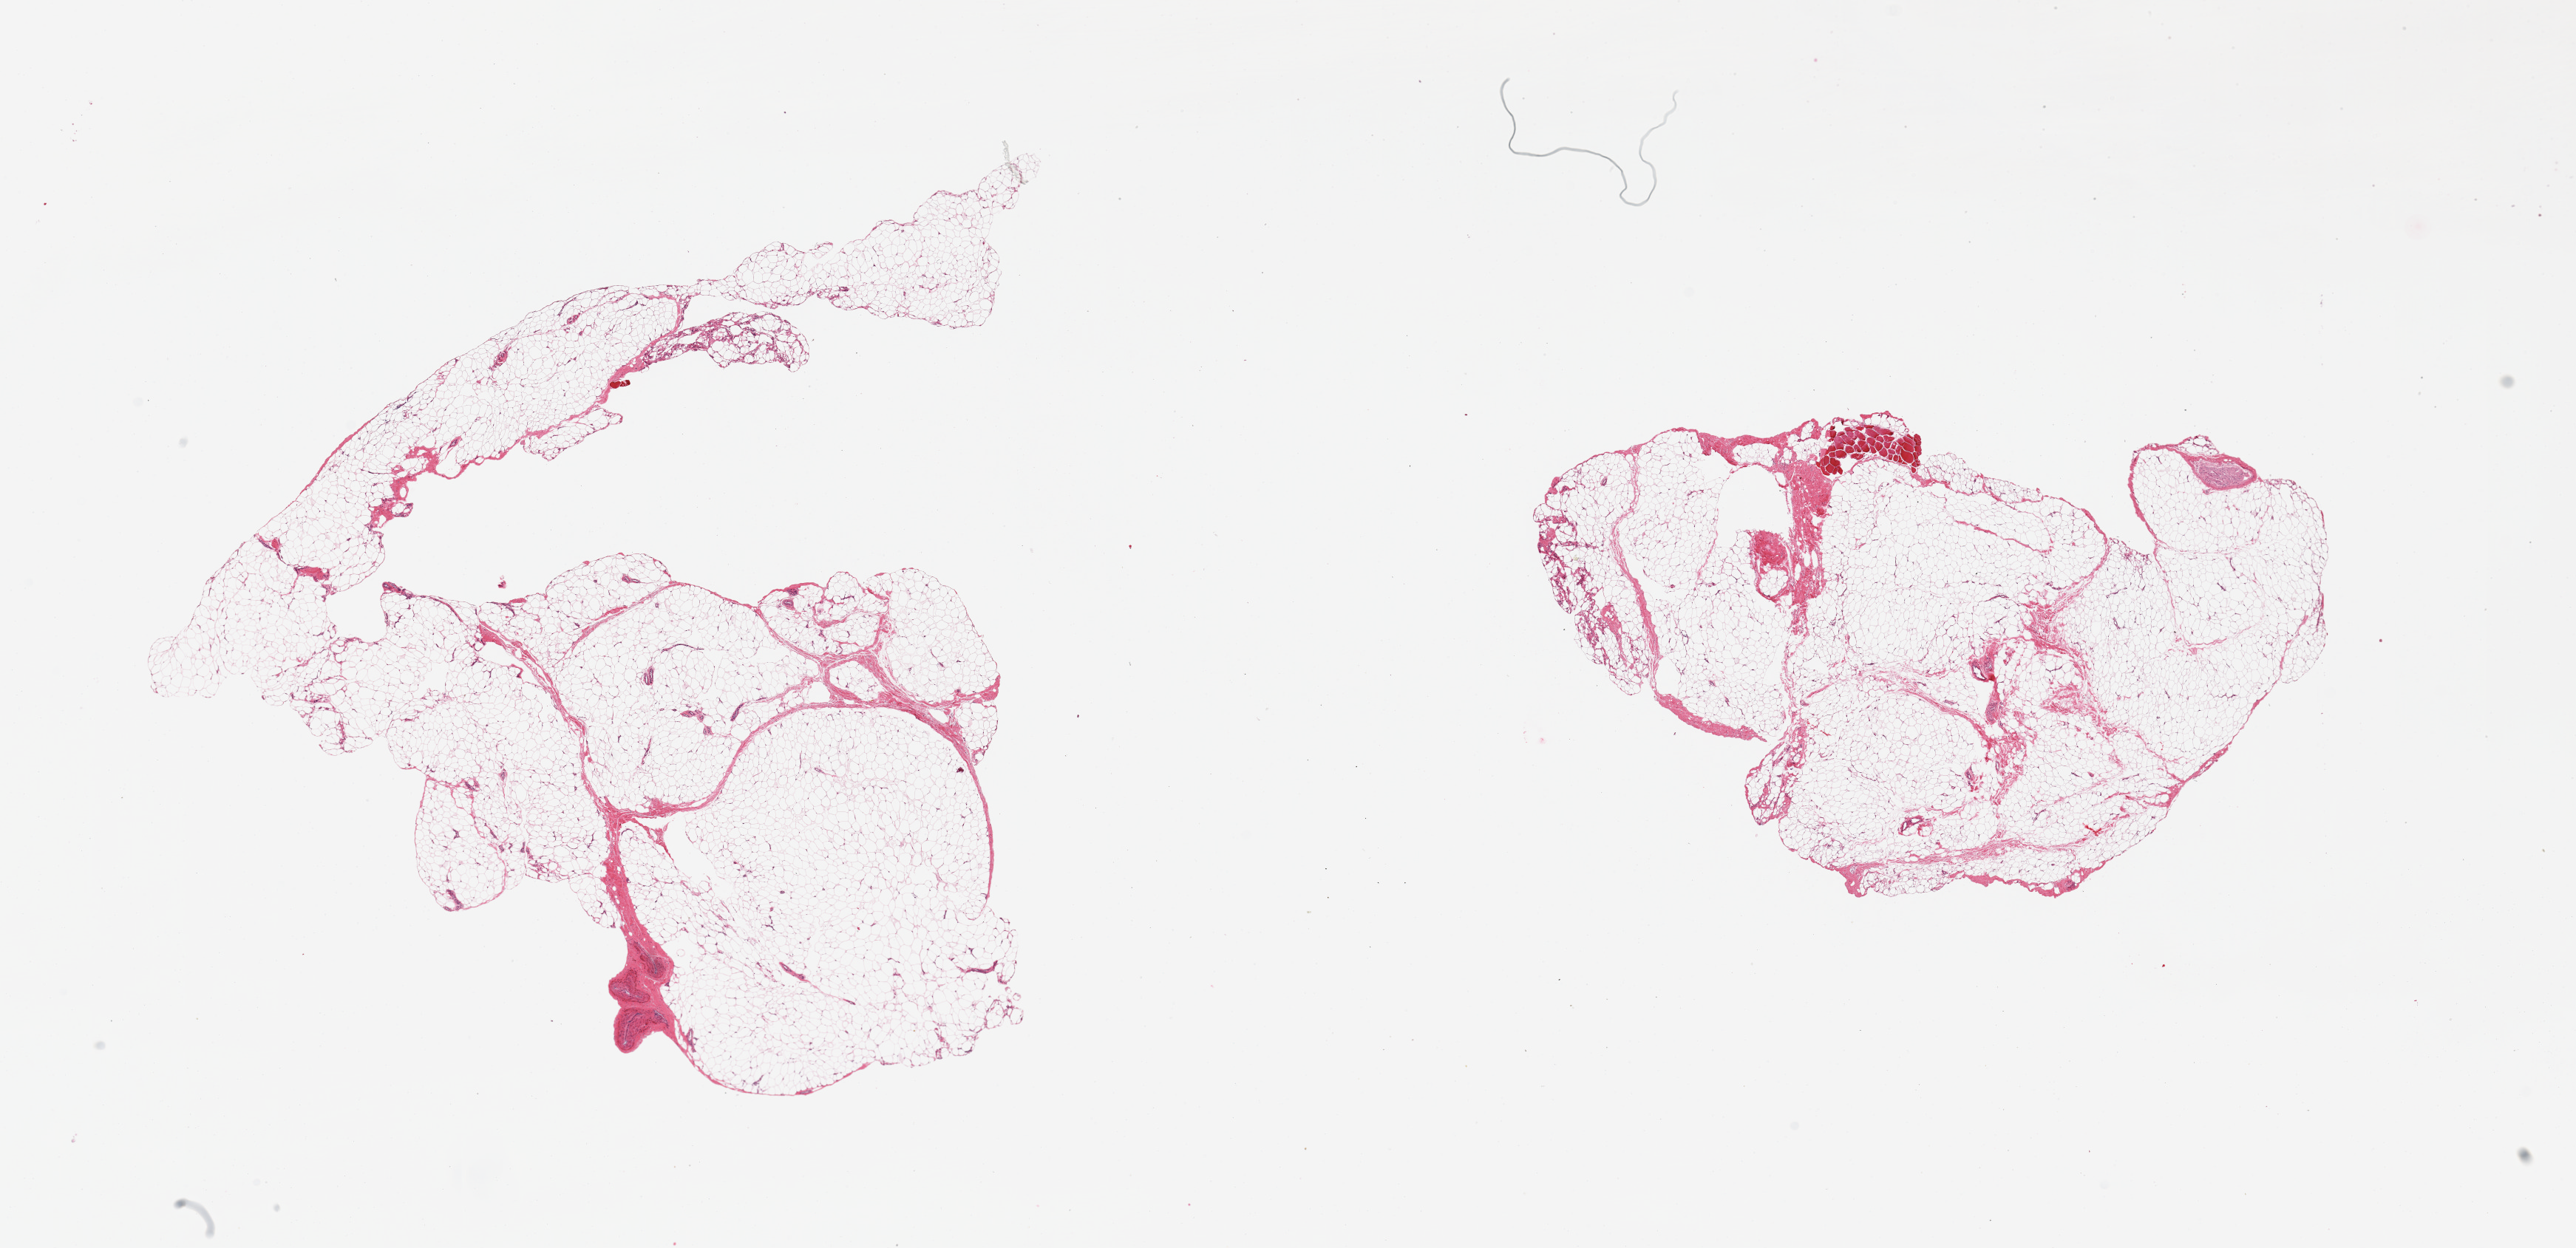
Haematoxylin and eosin whole-slide image, whole scanned area (about 27.6 x 13.4 mm, acquisition: 20x scan) shown as a low-resolution overview. PAXgene-fixed paraffin-embedded (PFPE) section. Target tissue: adipose tissue. Tissue donor sample.
Pathologist's review note for this sample: 2 pieces; 1 mm focus of skeletal muscle on 1 piece.